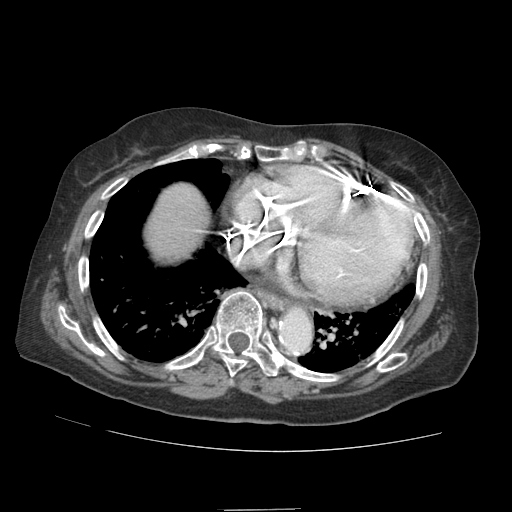
Contrast-enhanced abdominal CT (liver protocol), one axial slice. Position 82 of 89 along the scan axis. Reconstruction kernel STANDARD. 140 kVp. Soft-tissue window (W 400 / L 40 HU). 2.5 mm slice thickness. 512 × 512 image matrix. From the clinical record (not read from this slice): diagnosis: hepatocellular carcinoma (patient treated with transarterial chemoembolisation; whether this scan precedes or follows treatment is not stated here); TNM stage (as recorded): Stage-II; Child-Pugh class: A; tumour differentiation: moderately differentiated; tumour nodularity: multinodular.
Structures marked on this image (semi-automatic segmentation, software-assisted and operator-edited):
- abdominal aorta: bounding box [x1, y1, x2, y2] px = [280, 309, 310, 350]
- liver parenchyma outside the tumour (the mass and vessels are separate outlines, so this box may not span the whole liver): [146, 182, 208, 258]